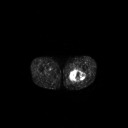
FDG PET of an extremity soft-tissue mass (from a PET/CT study), one axial slice. Slice 252 of 267 in the series (ordered by position). 3.27 mm slice thickness. 128 × 128 image matrix, field of view 700 × 700 mm. Male patient, age 44 years. From the clinical record (not read from this slice): histological type: undifferentiated pleomorphic liposarcoma; grade: high; site of the primary tumour: left thigh.
Annotated regions visible in this slice (expert contour drawn on MRI and transferred to this co-registered scan by the dataset authors):
- gross tumour volume including surrounding oedema: bounding box (x1, y1, x2, y2) in pixels: (68, 69, 85, 83)
- gross tumour volume (mass): (70, 70, 85, 81)